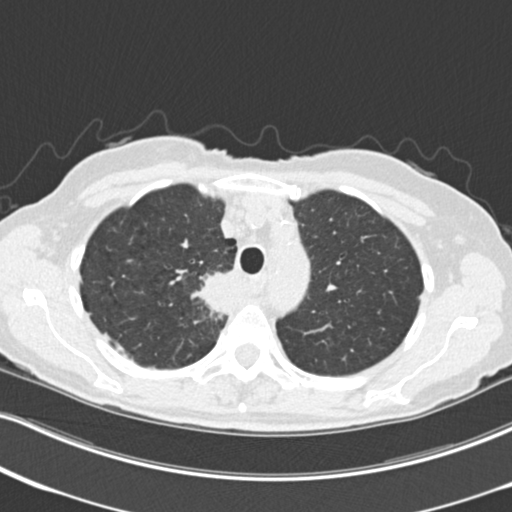
Low-dose screening chest CT, one axial slice; reconstruction kernel B30f; lung window (W 1500 / L -600 HU); 2 mm slice thickness; 512 × 512 image matrix, field of view 322 × 322 mm.
Structures marked on this image (manually delineated by an expert):
- lesion 1 (tumor, mediastinum): bounding box [x1, y1, x2, y2] px = [192, 271, 232, 318]